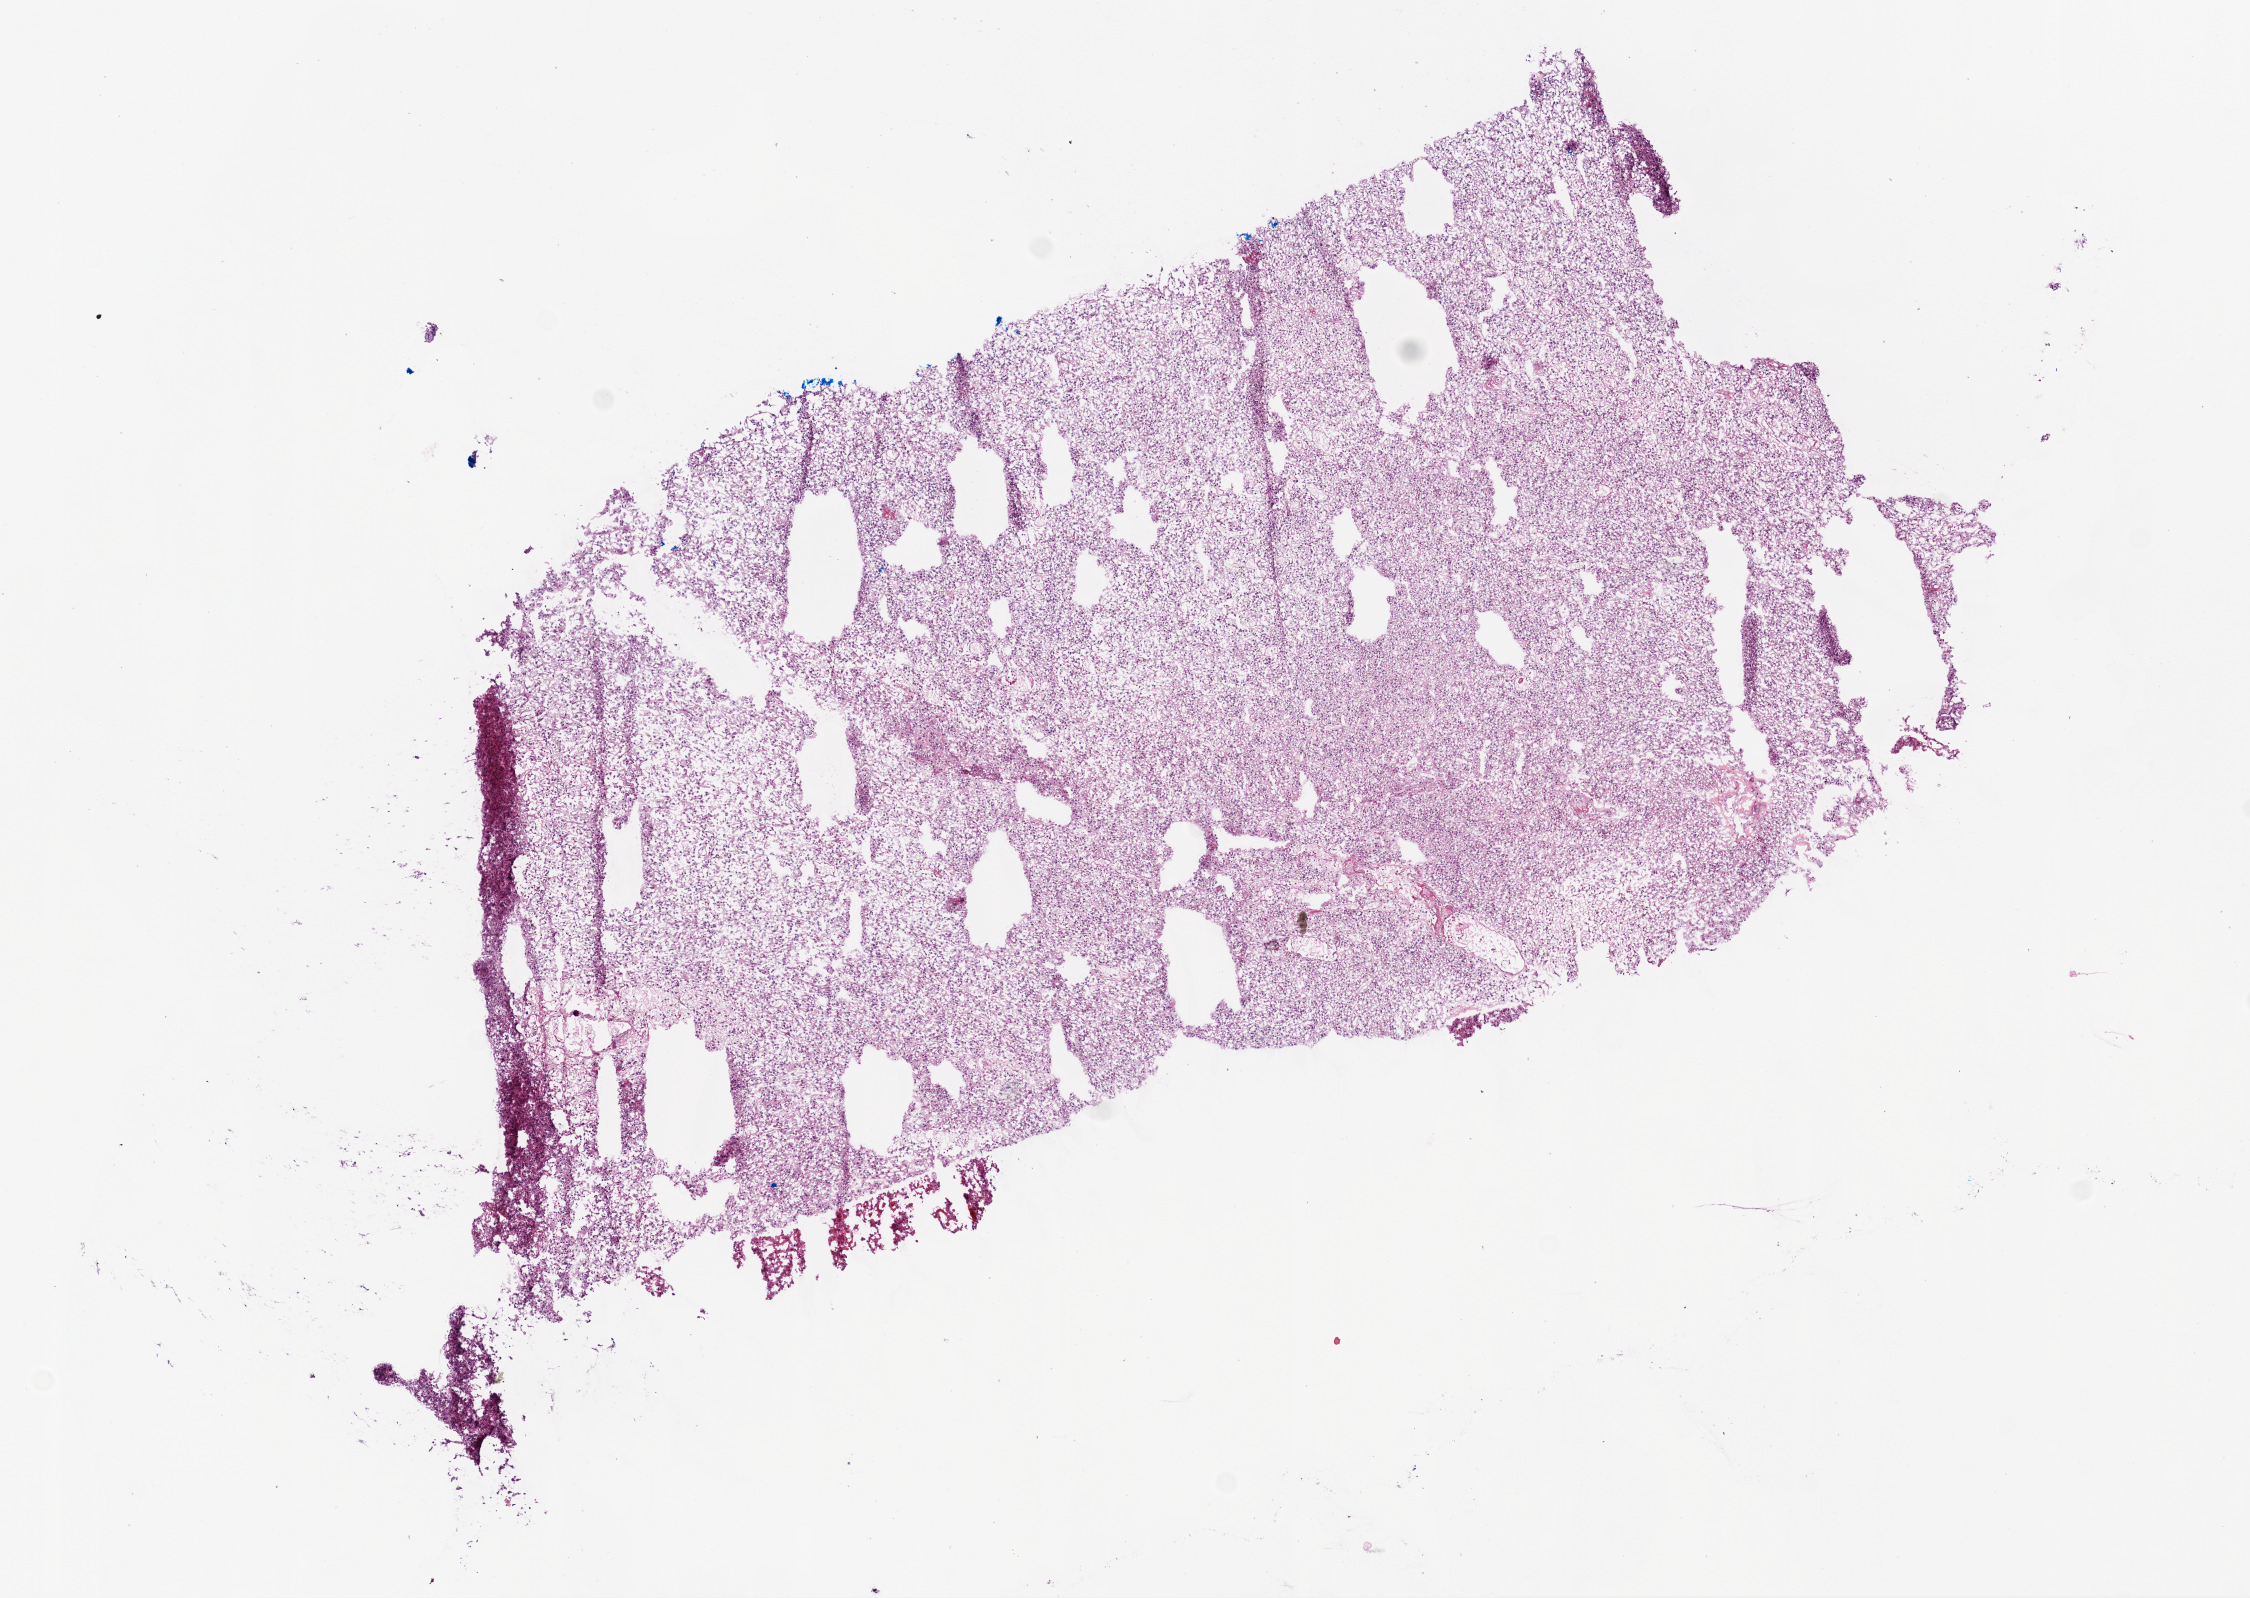
Hematoxylin and eosin (H&E) stained whole-slide image — whole scanned area (about 9.0 x 6.4 mm, acquisition: 20x scan) shown as a low-resolution overview. Frozen section. Primary tumour sample from the brain. Female, age 76 years at initial diagnosis. Slide review estimates, as recorded: tumour cells 90%, tumour nuclei 95%, normal cells 0%, stromal cells 5%, necrosis 5%.
Histologic diagnosis: Glioblastoma.